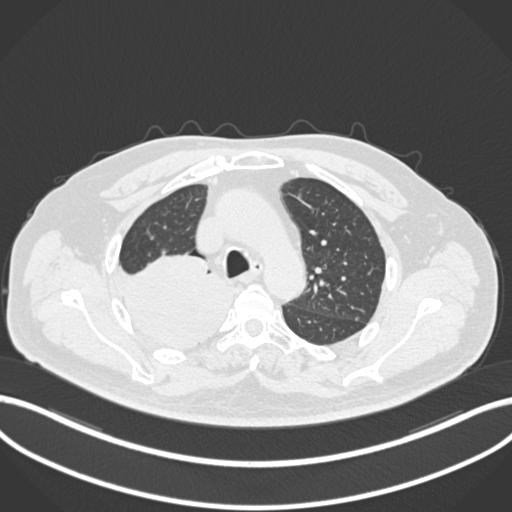
Chest CT, one axial slice; position 151 of 218 along the scan axis; 120 kVp; lung window (W 1500 / L -600 HU); 1 mm slice thickness; 512 × 512 image matrix. Male patient, age 68 years. Case-level facts recorded for this patient, not image findings: clinical TNM (as recorded): T2a N0 M0.
Annotated regions visible in this slice (rectangle marked by the reading radiologist):
- lung tumour (recorded histology: adenocarcinoma): bounding box (x1, y1, x2, y2) in pixels: (112, 249, 229, 351)